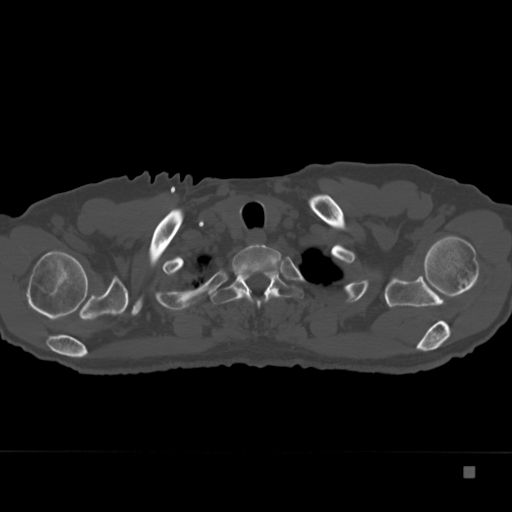
CT including the spine, one axial slice; position 306 of 332 along the scan axis; 120 kVp; bone window (W 1800 / L 400 HU); 1.5 mm slice thickness; 512 × 512 image matrix. Male patient, age 72 years. From the clinical record (not read from this slice): primary cancer: skeletal.
Structures marked on this image (semi-automatically segmented with operator editing):
- T1 vertebra: box from (x=232, y=244) to (x=282, y=299) px
- T2 vertebra: (x=211, y=266)–(x=304, y=309)